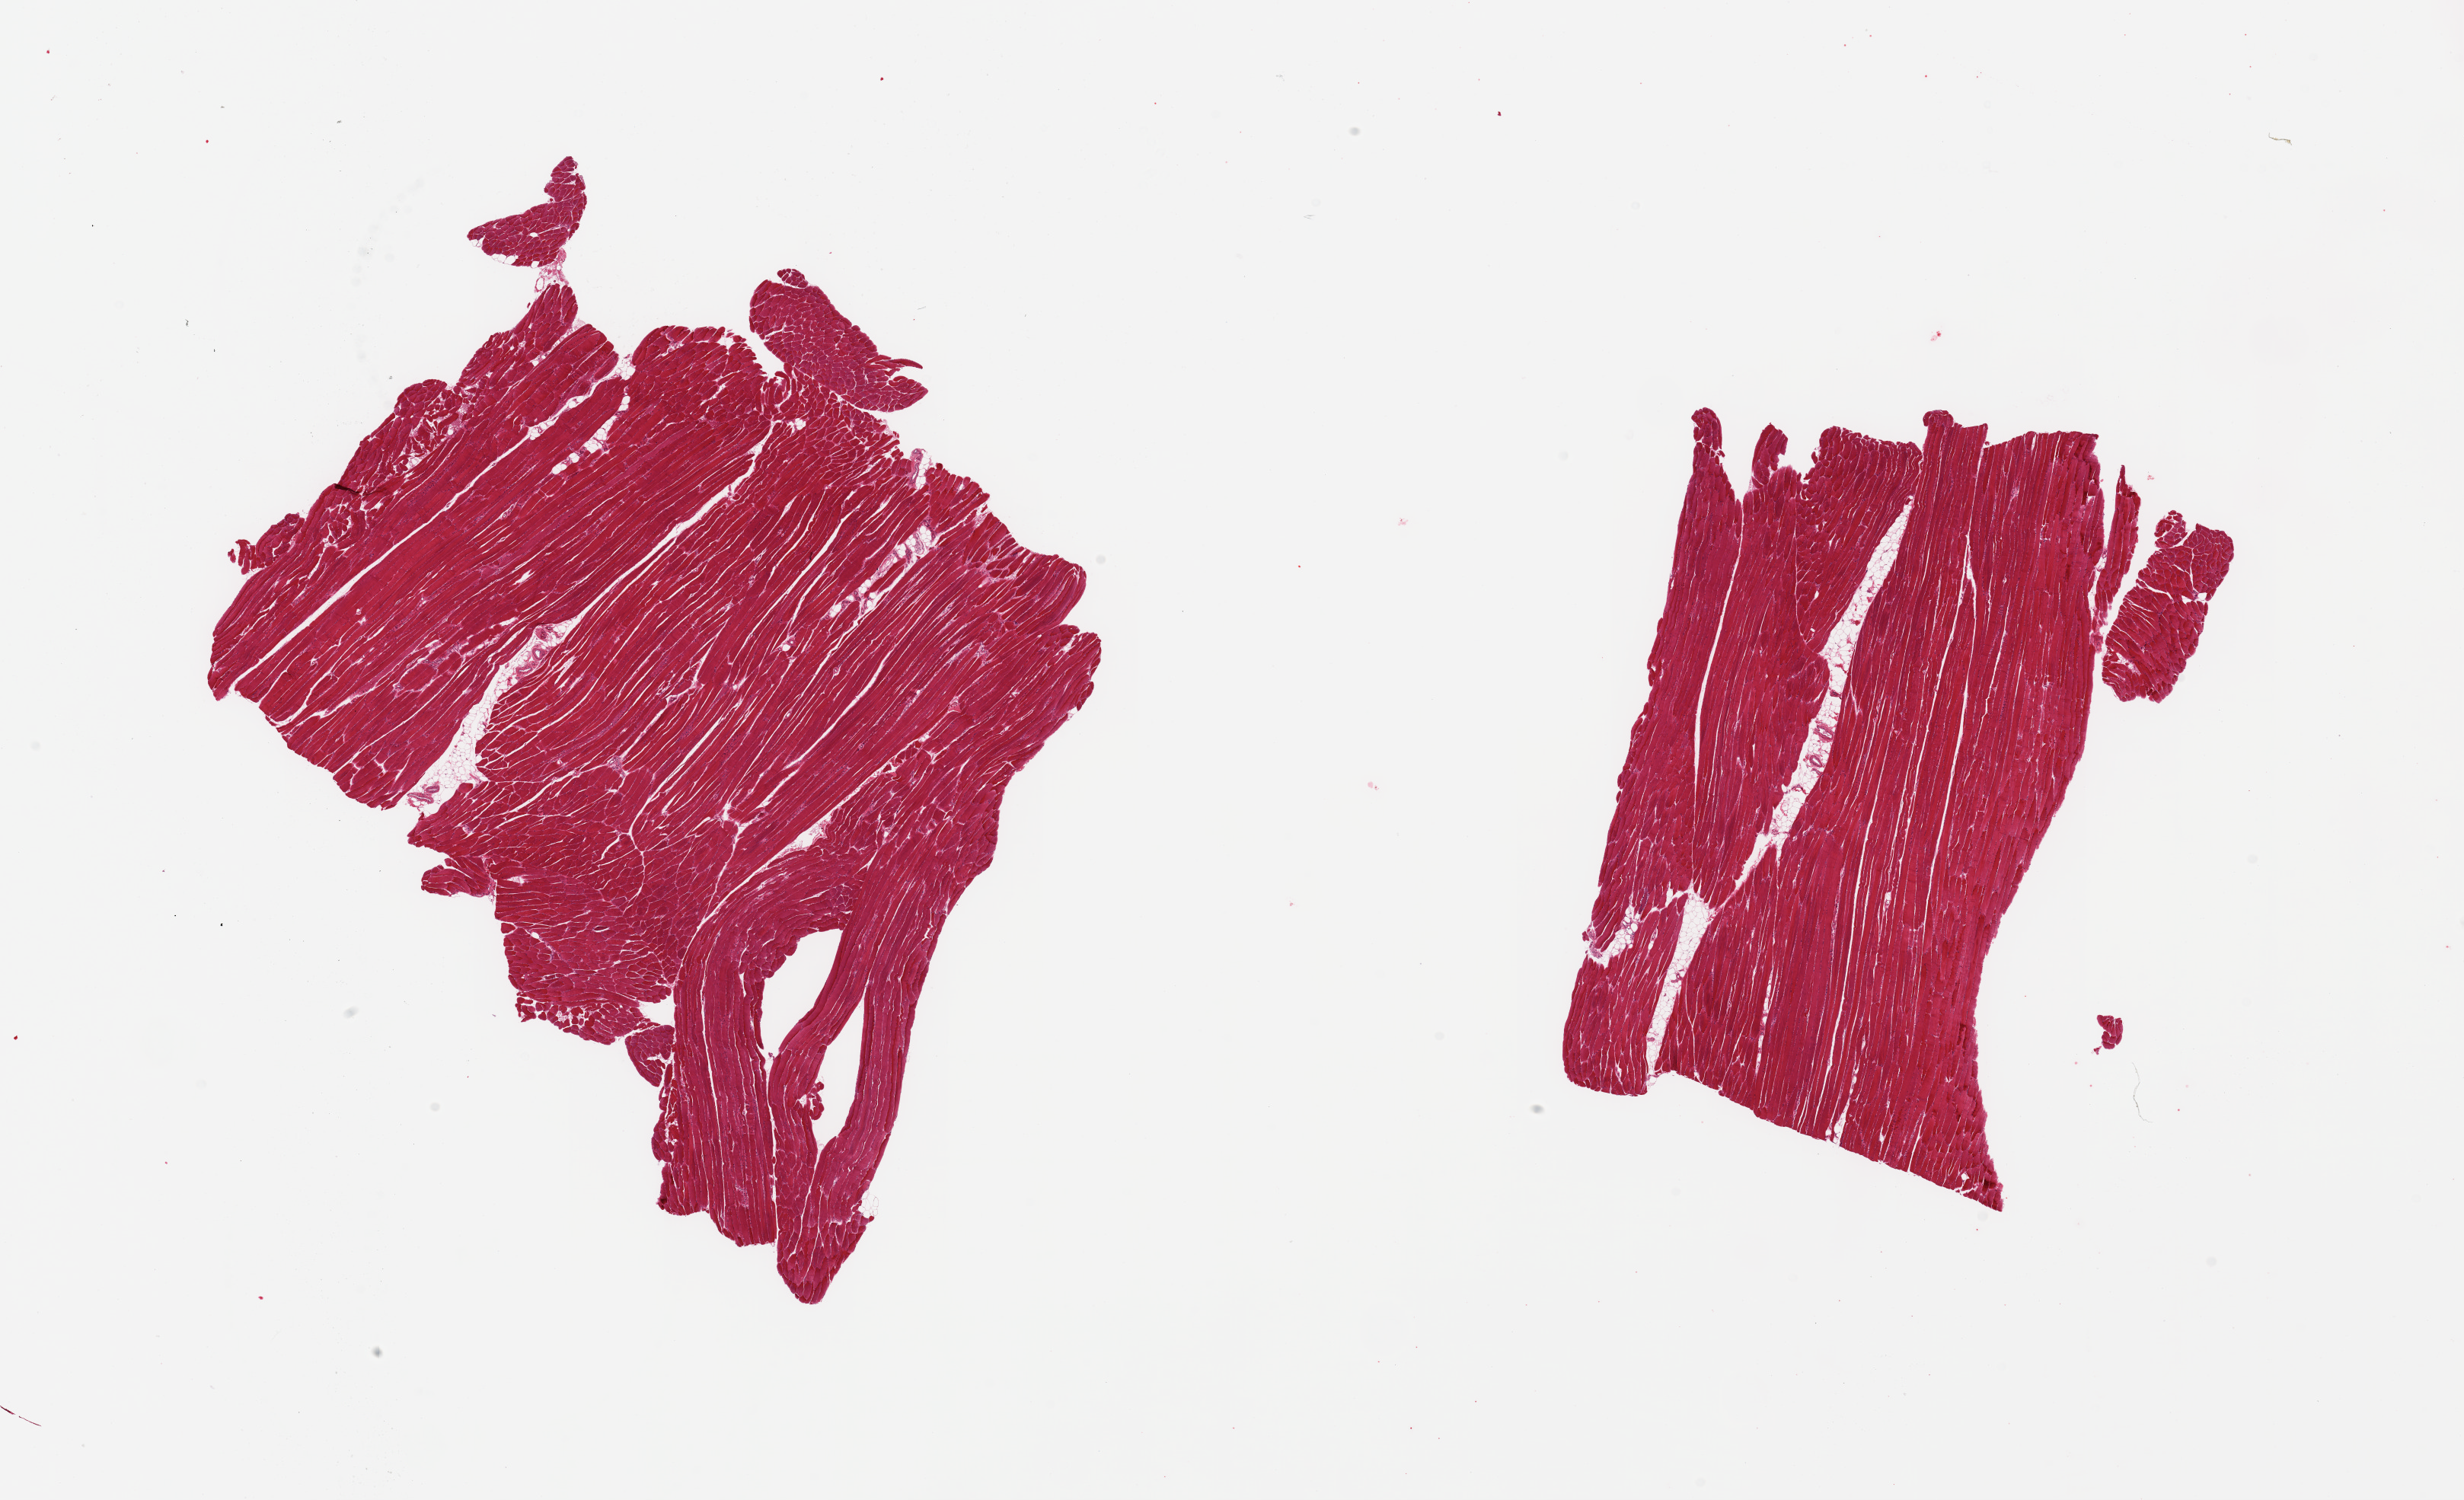
Hematoxylin and eosin (H&E) whole-slide image — shown as a low-resolution overview of the whole scanned area (about 25.6 x 15.6 mm), PAXgene-fixed, paraffin-embedded tissue, target tissue: skeletal muscle, tissue donor sample. Donor: female.
Review note (as recorded): 2 pieces; minimal internal fat.